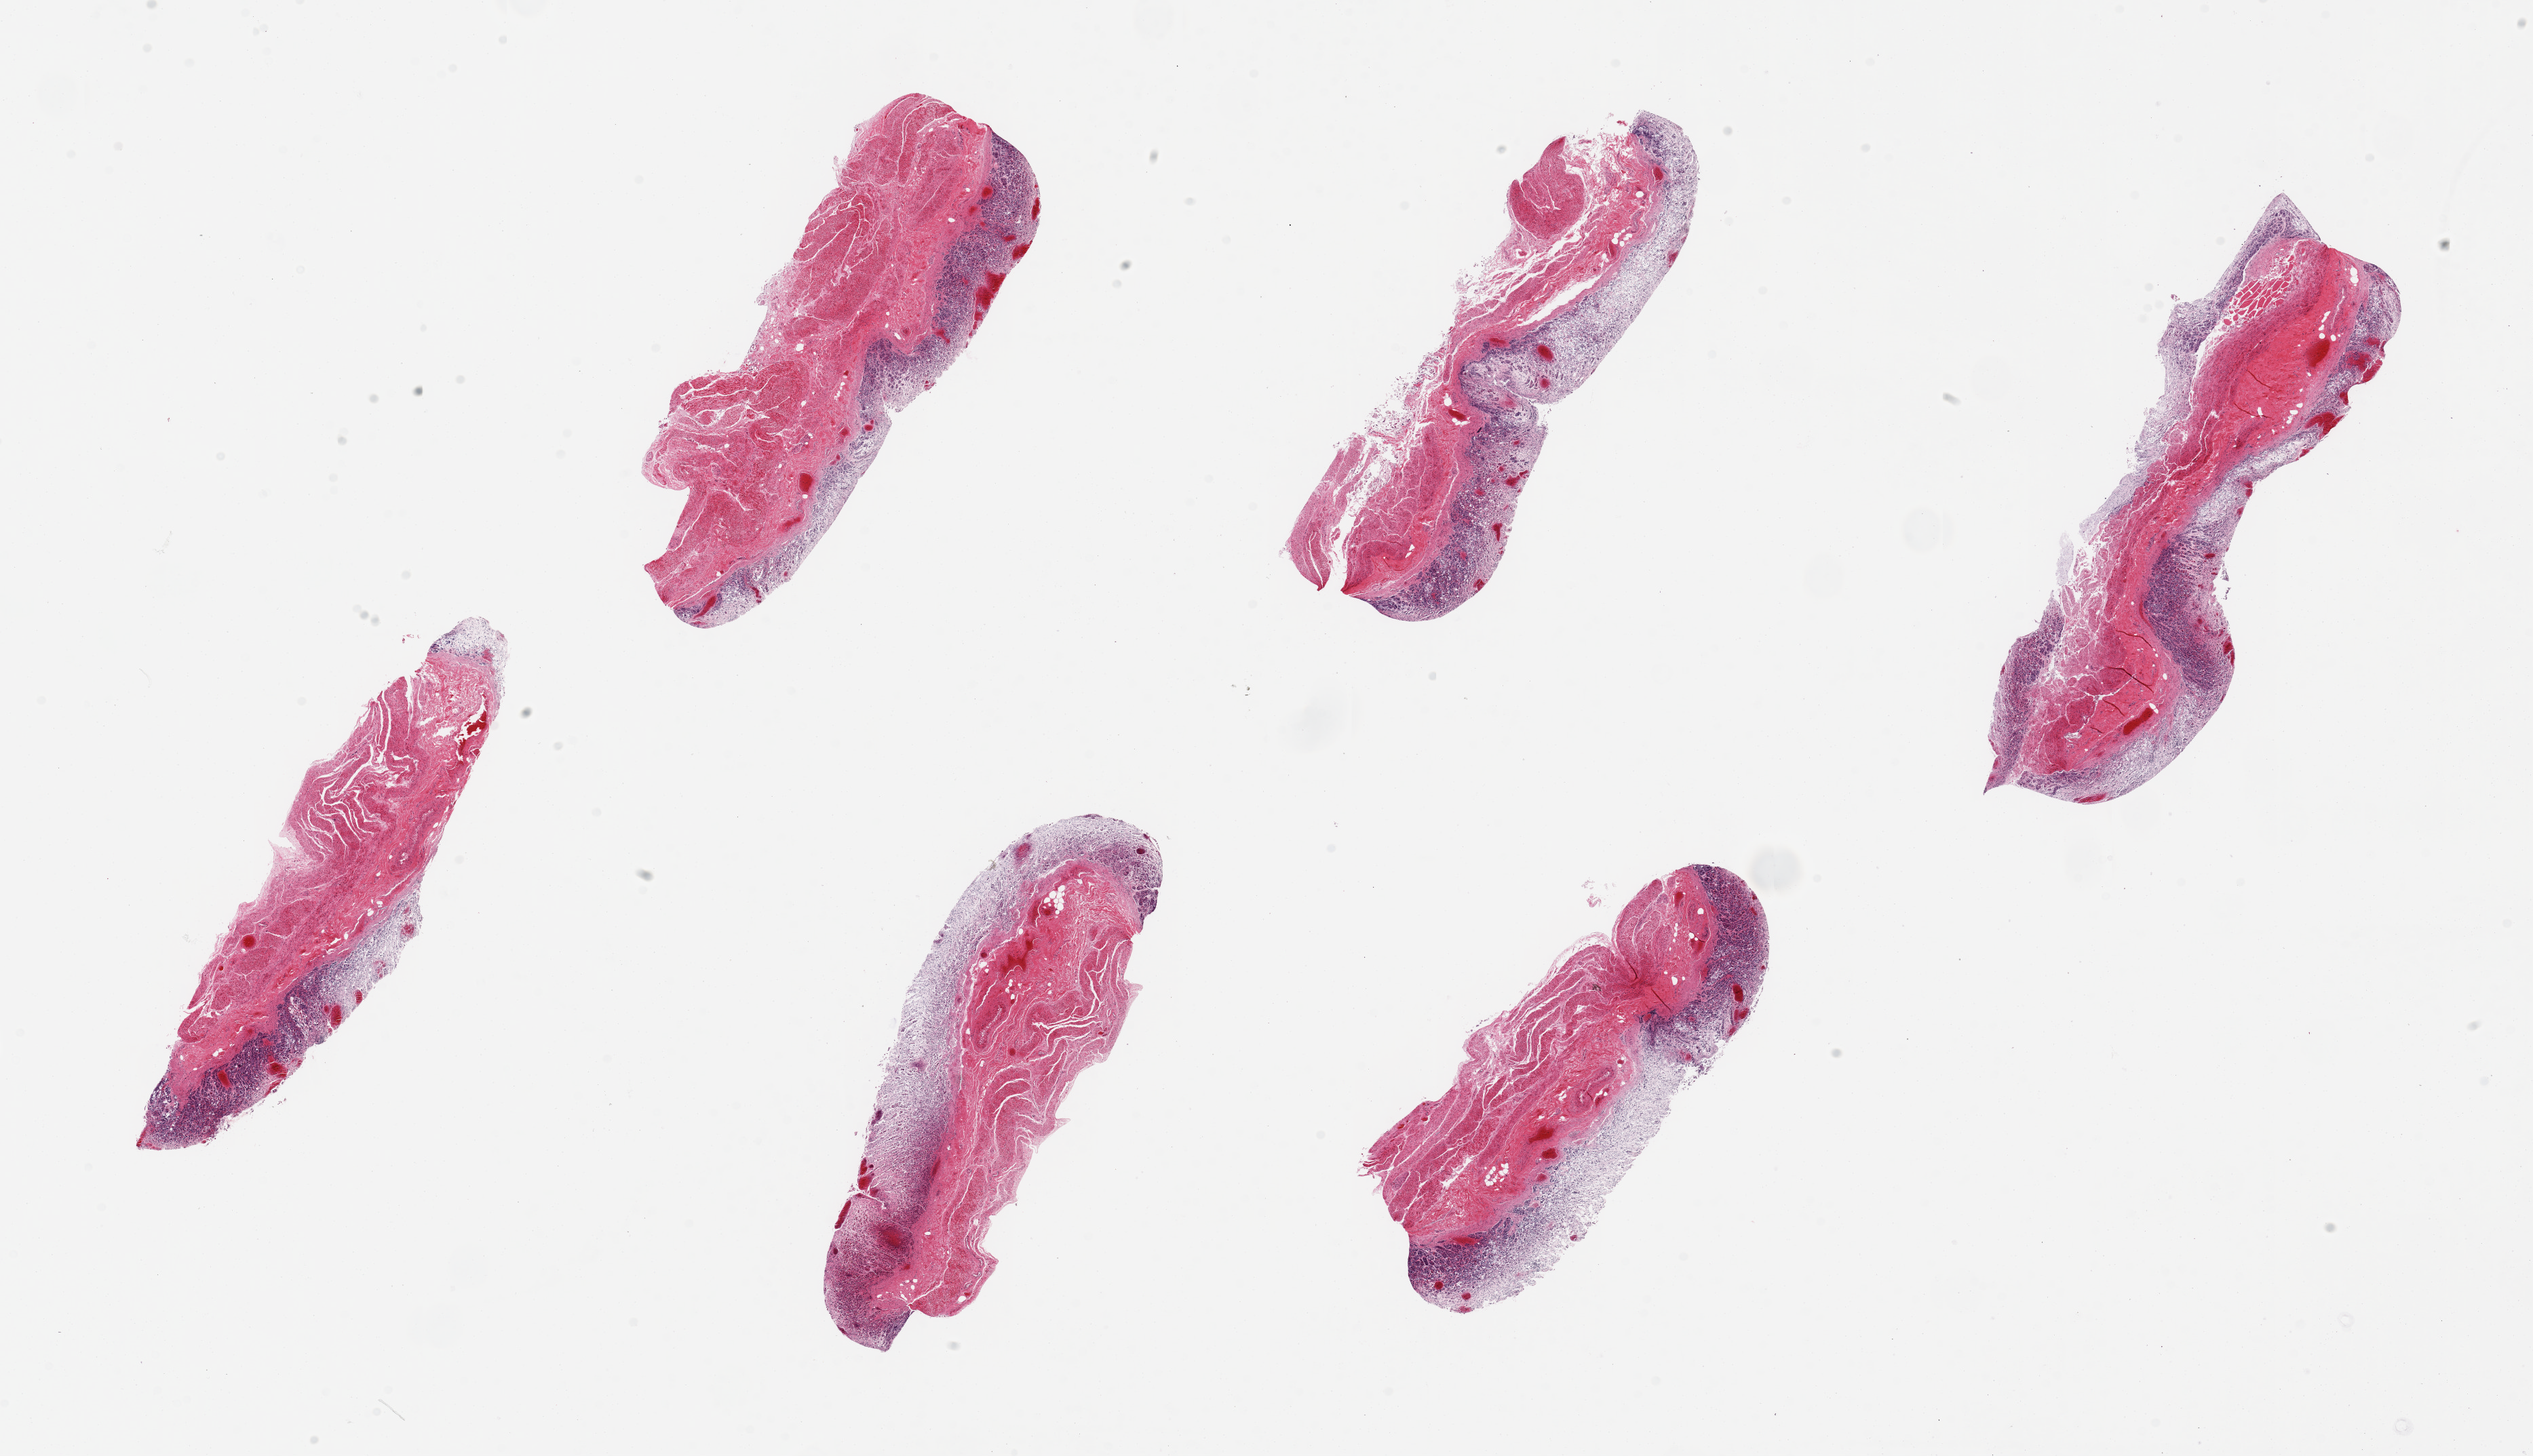
Digitized H&E-stained section, a low-resolution overview of the entire scanned area, about 29.5 x 17.0 mm (slide scanned at 20x). PAXgene-fixed paraffin-embedded (PFPE) section. Sampled site (target tissue): stomach. Donor tissue sample. Donor: female.
Reviewer comment on this tissue sample: 6 pieces. up to 8x3mm; mucosa = 3; muscle = 2.